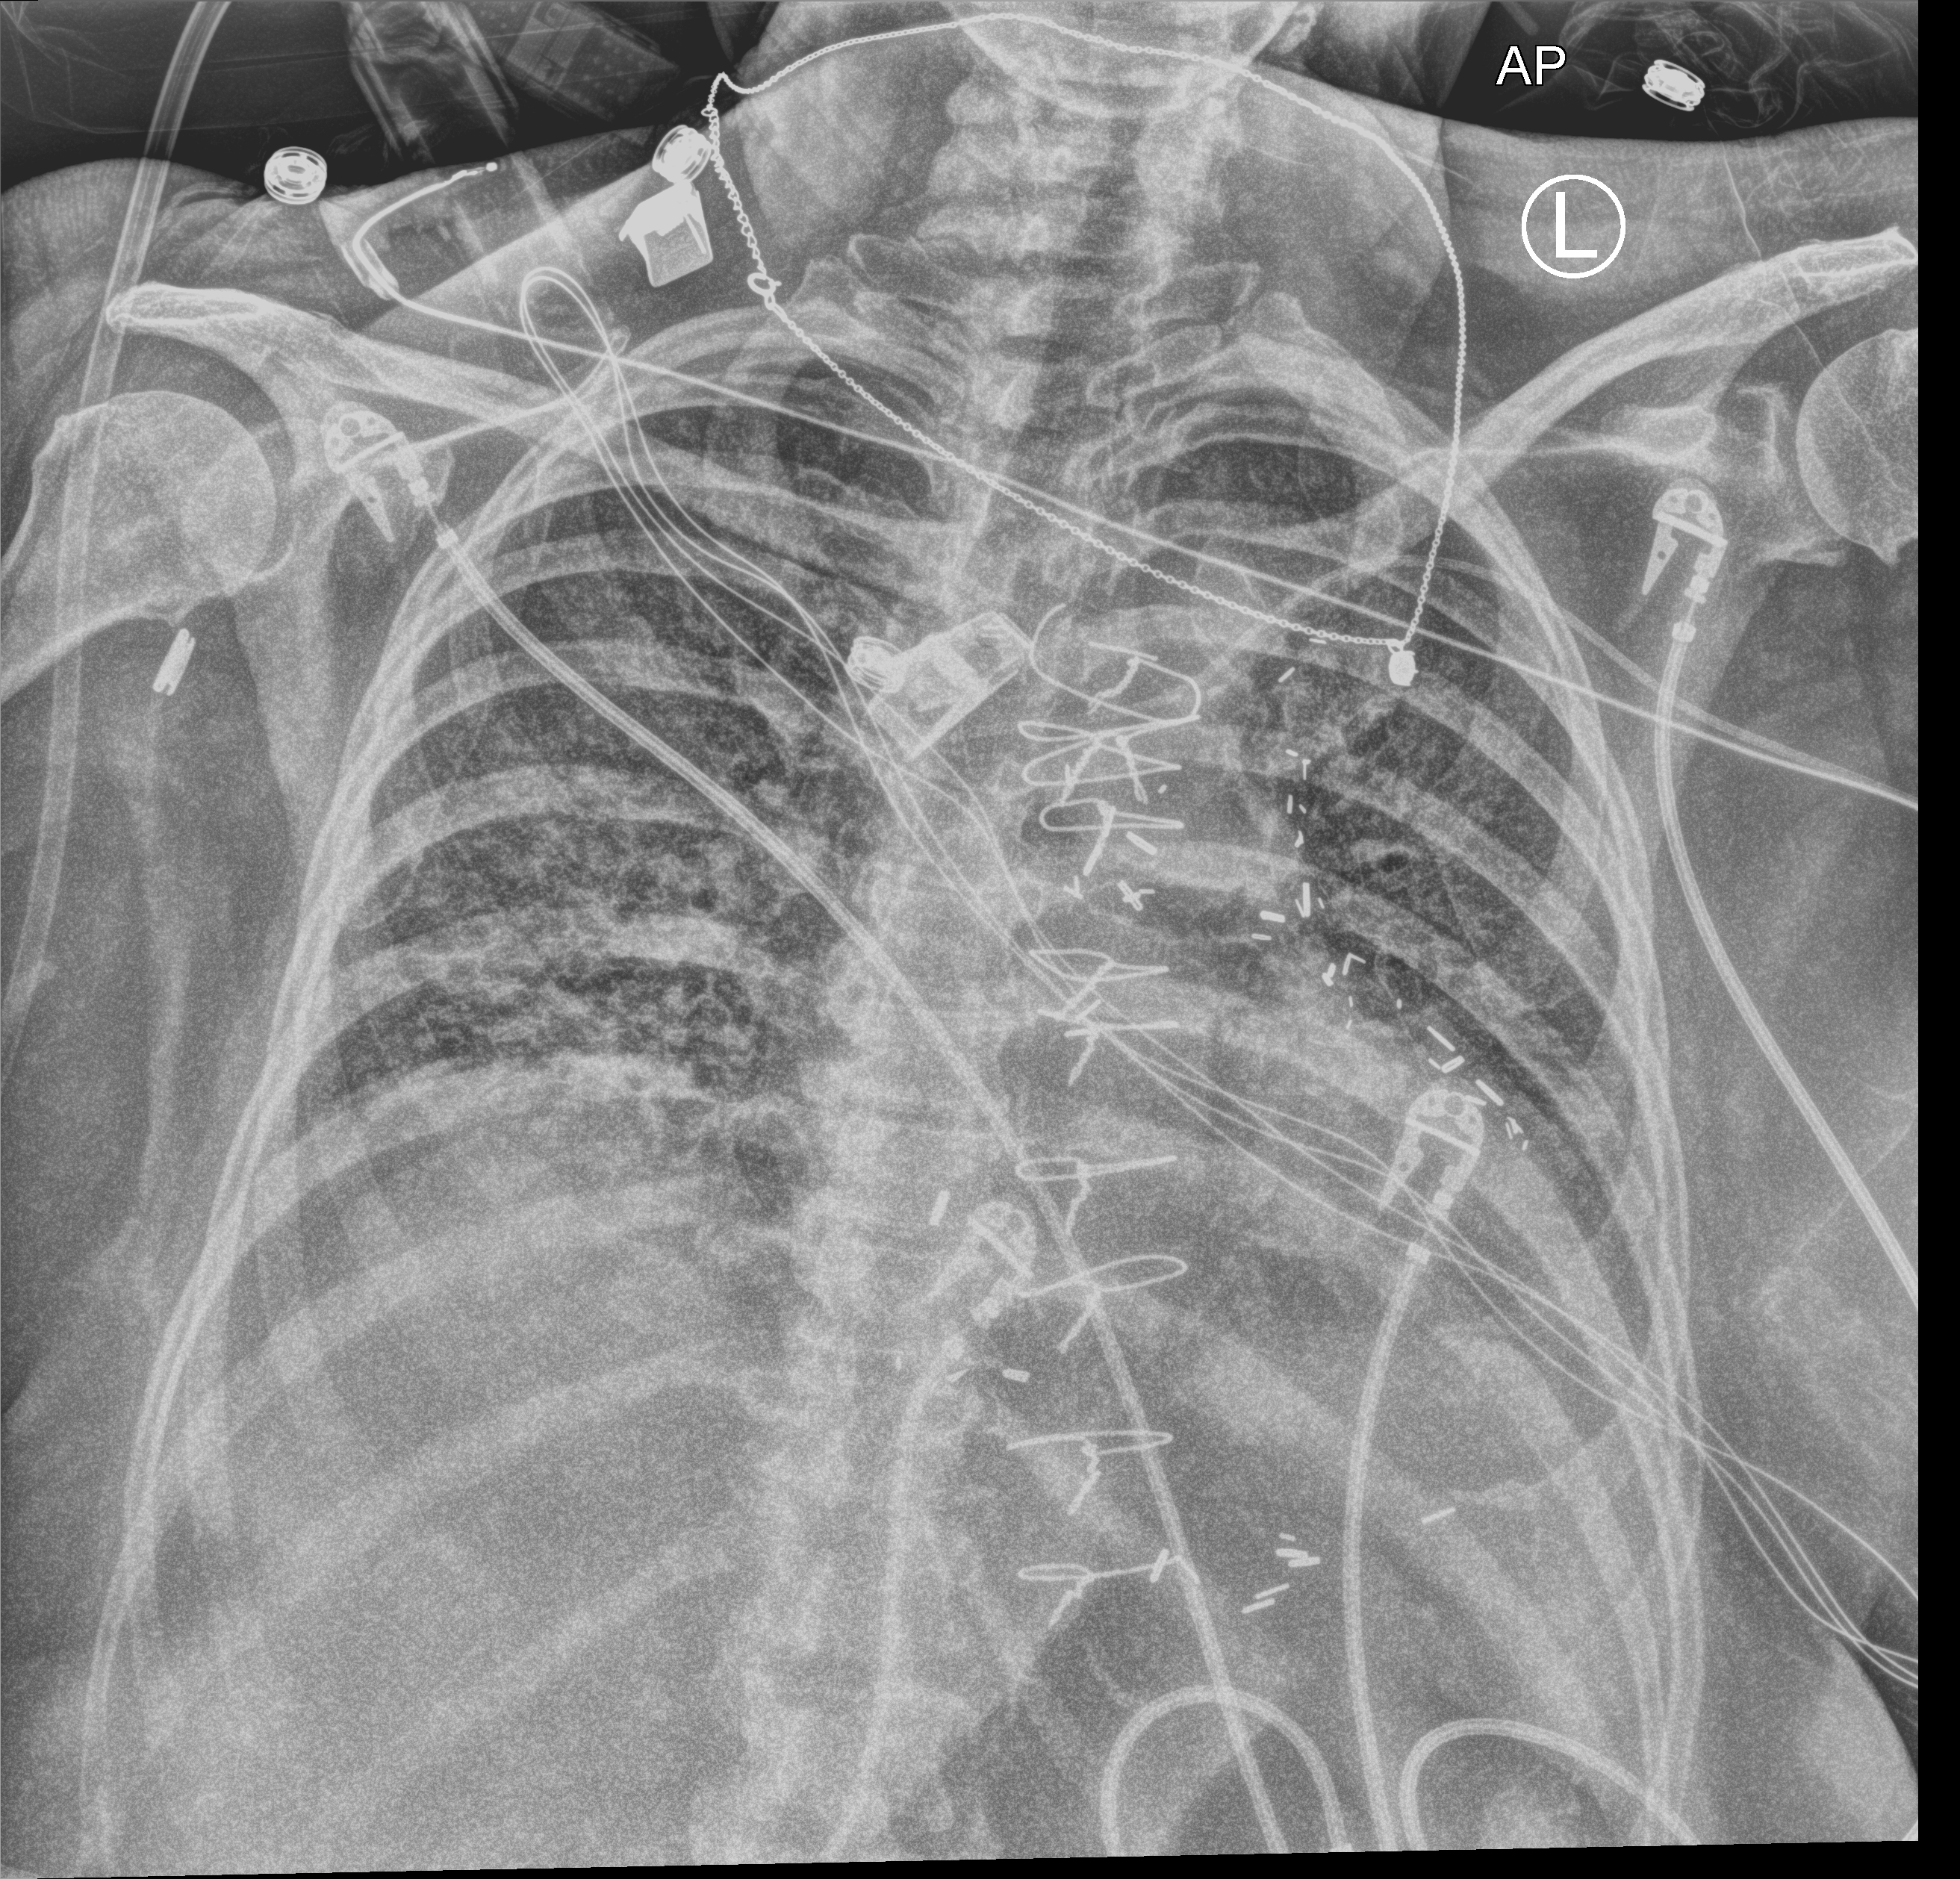
Chest X-ray (portable); anteroposterior (AP) projection. Female patient hospitalised with COVID-19, age 60–74 years.
Admission-level facts for this patient (not findings on this image; timing relative to this image not recorded):
- admitted to intensive care during this hospital stay: yes